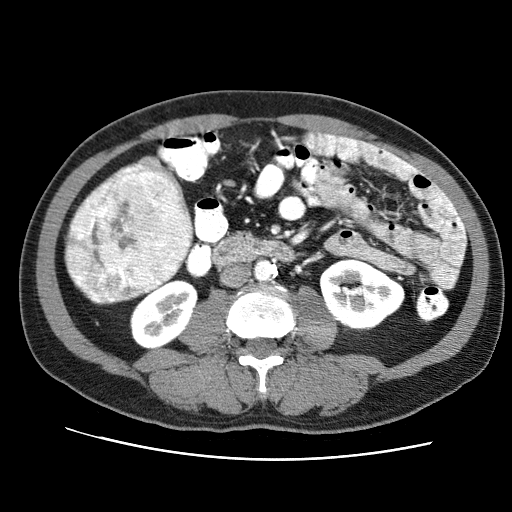
Contrast-enhanced abdominal CT (liver protocol), one axial slice; position 16 of 71 along the scan axis; reconstruction kernel STANDARD; 120 kVp; soft-tissue window (W 400 / L 40 HU); 2.5 mm slice thickness; 512 × 512 image matrix, field of view 360 × 360 mm. From the clinical record (not read from this slice): diagnosis: hepatocellular carcinoma (patient treated with transarterial chemoembolisation; whether this scan precedes or follows treatment is not stated here); TNM stage (as recorded): Stage-II; Child-Pugh class: A.
Outlined on this slice (semi-automatically segmented with operator editing):
- liver parenchyma outside the tumour (the mass and vessels are separate outlines, so this box may not span the whole liver): bounding box <64,155,191,301> (left, top, right, bottom; pixels)
- mass: <64,165,192,304>
- liver vessels: <146,168,148,170>